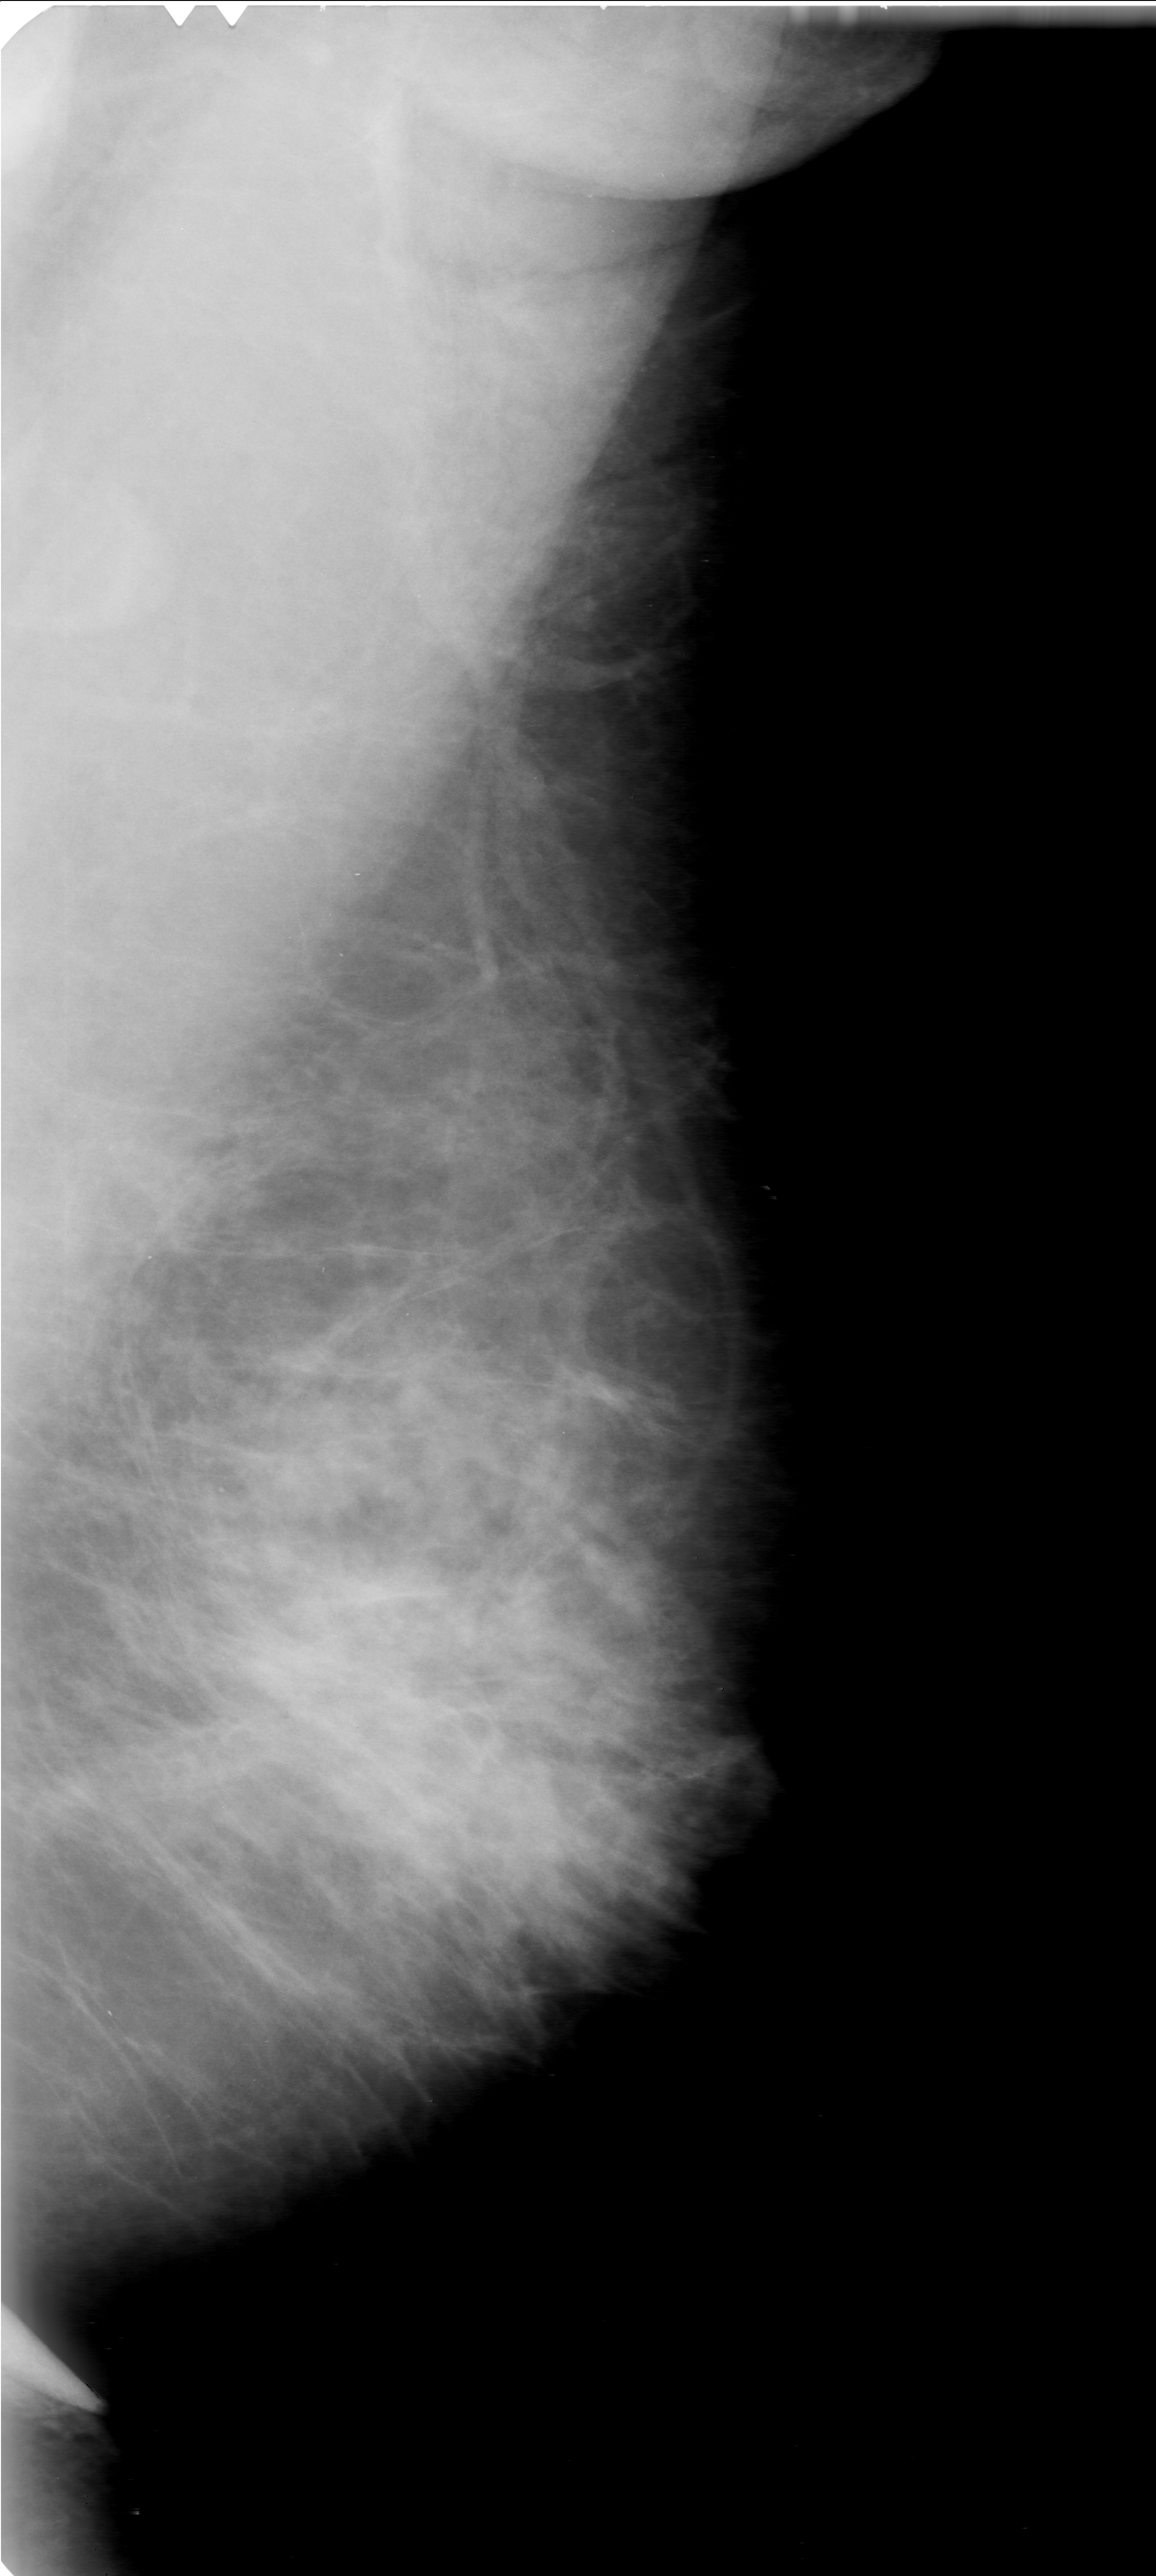
Digitized screen-film mammogram; left breast; mediolateral oblique (MLO) view; breast composition: heterogeneously dense (BI-RADS density category 3 of 4).
- Finding: mass, shape architectural distortion; BI-RADS assessment category 0 (incomplete: needs additional imaging); pathology result (as recorded, not read from the image): malignant.